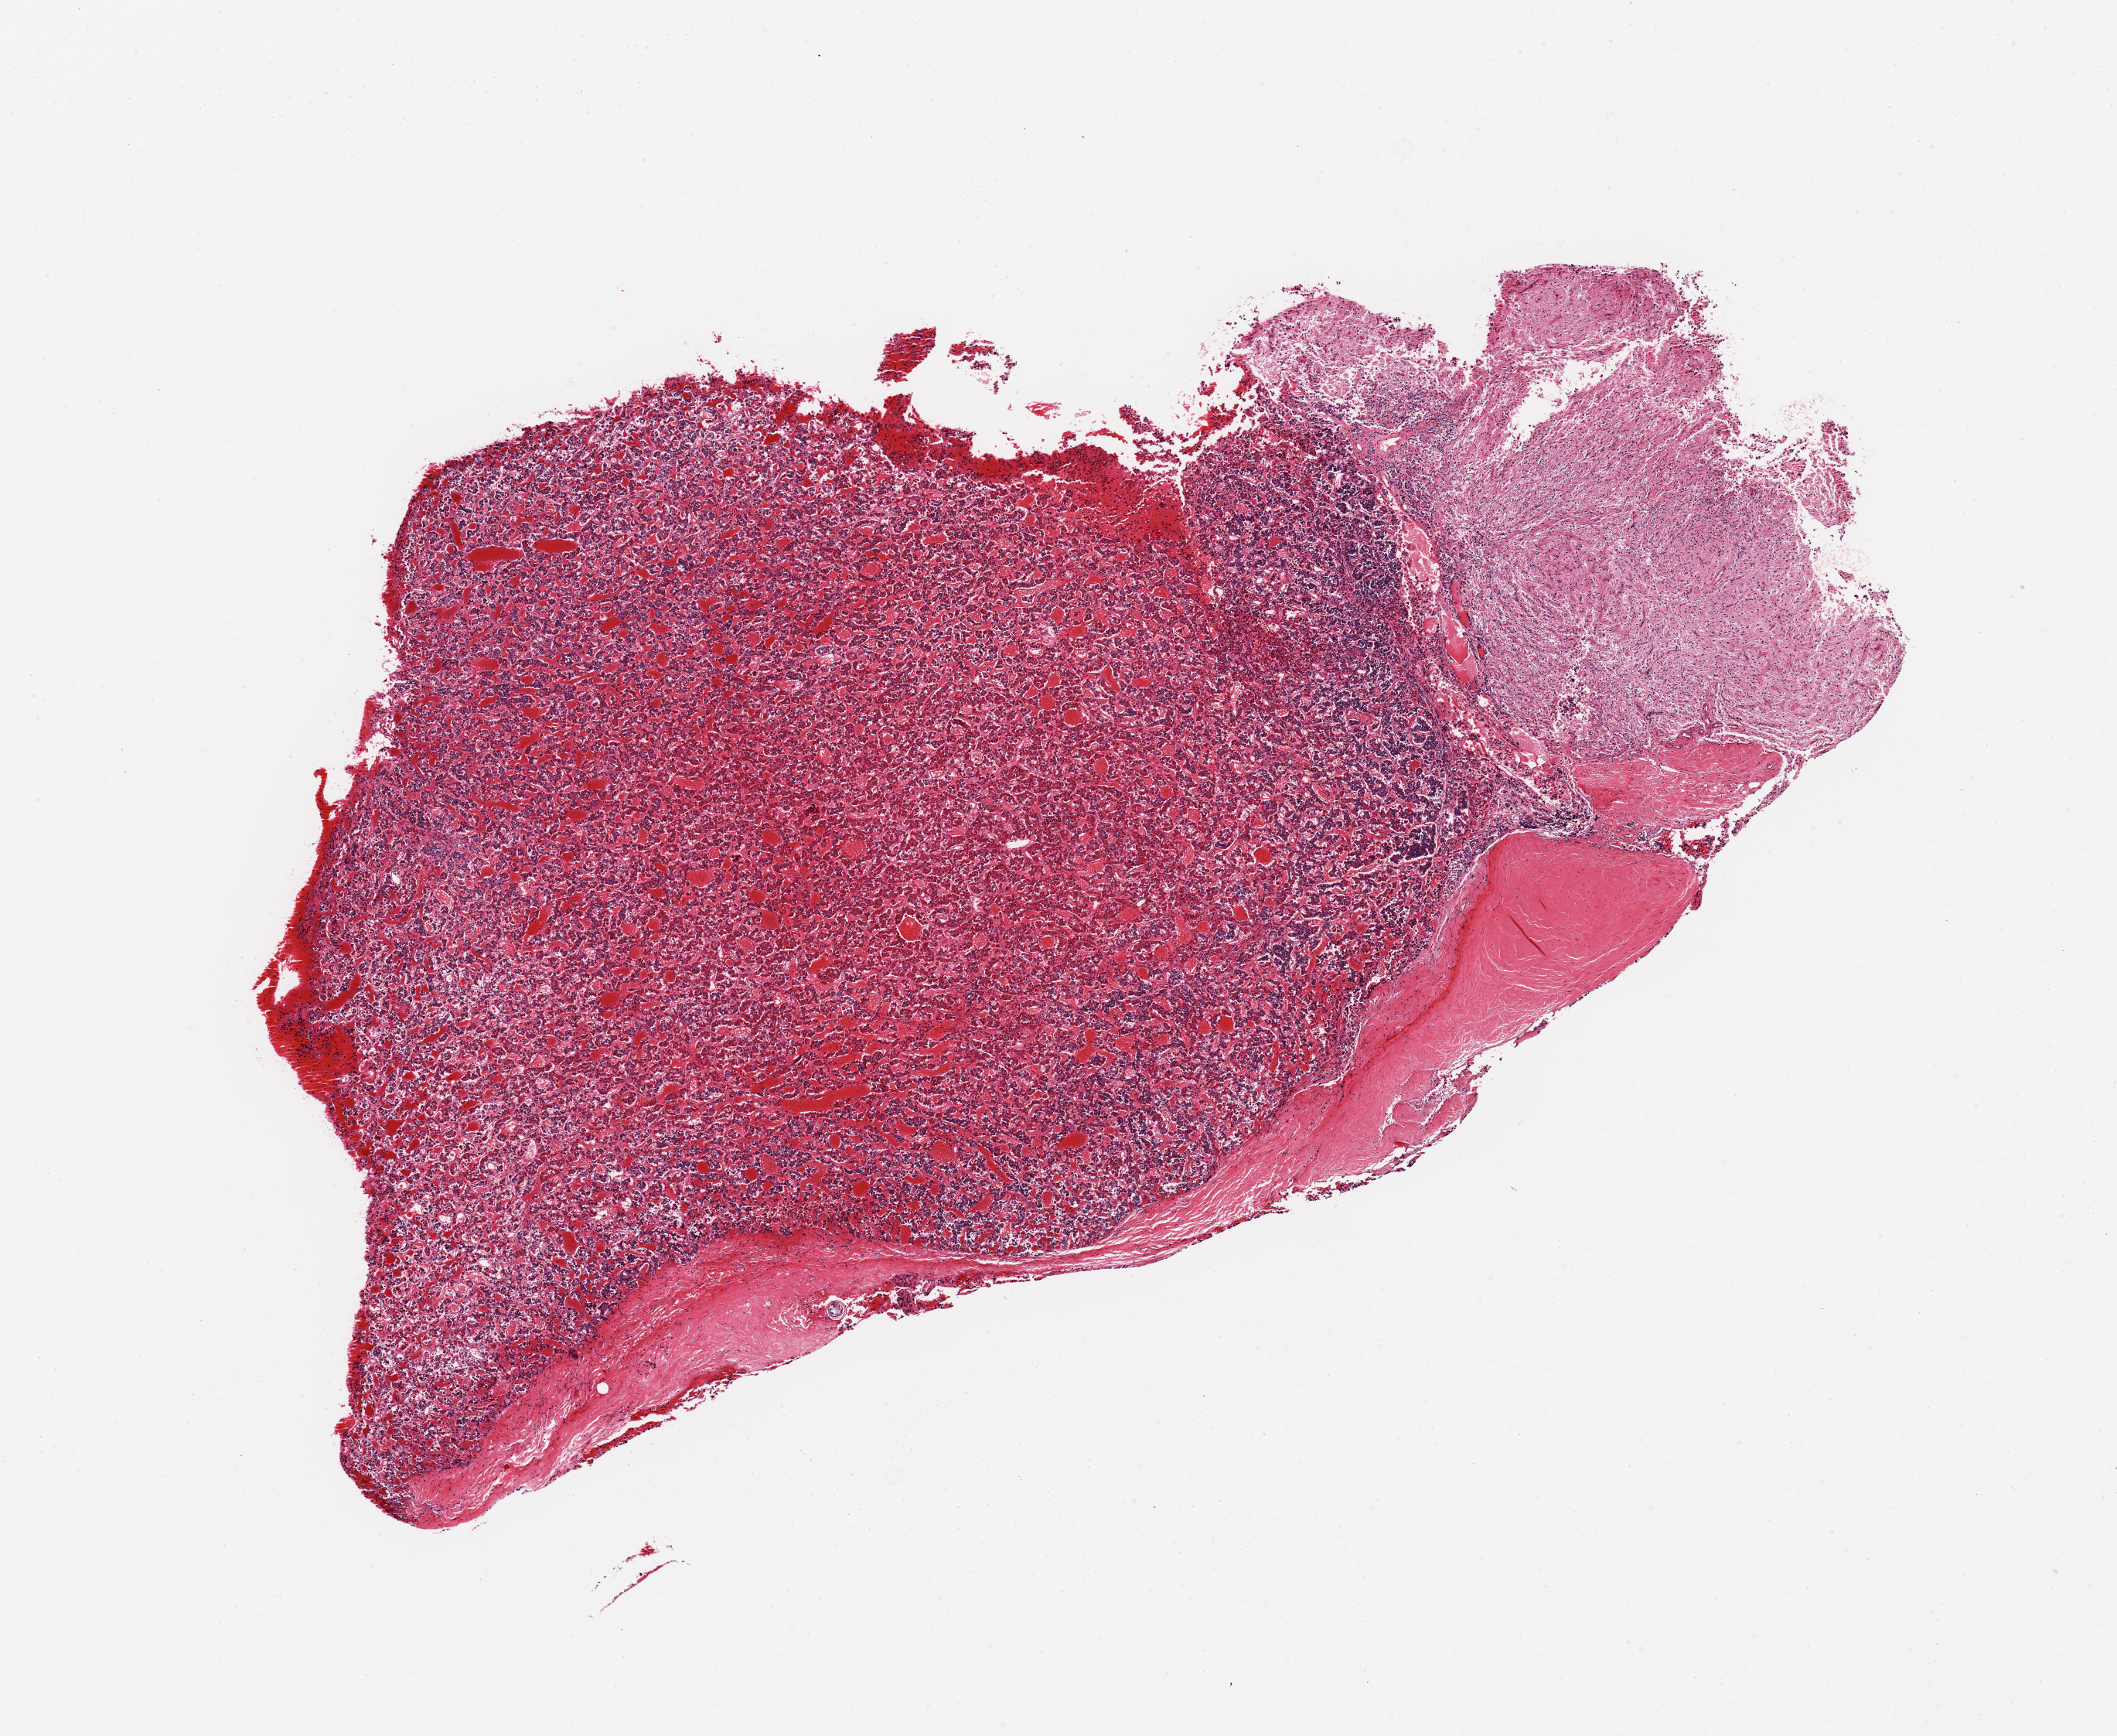
Whole-slide image, hematoxylin and eosin (H&E) stain, shown as a low-resolution overview of the whole scanned area (about 10.8 x 8.9 mm). PAXgene-fixed, paraffin-embedded tissue. Section of pituitary (target tissue). Tissue donor sample. Female donor.
Review note (as recorded): 1 piece; adenohypophysis and neurohypophysis.